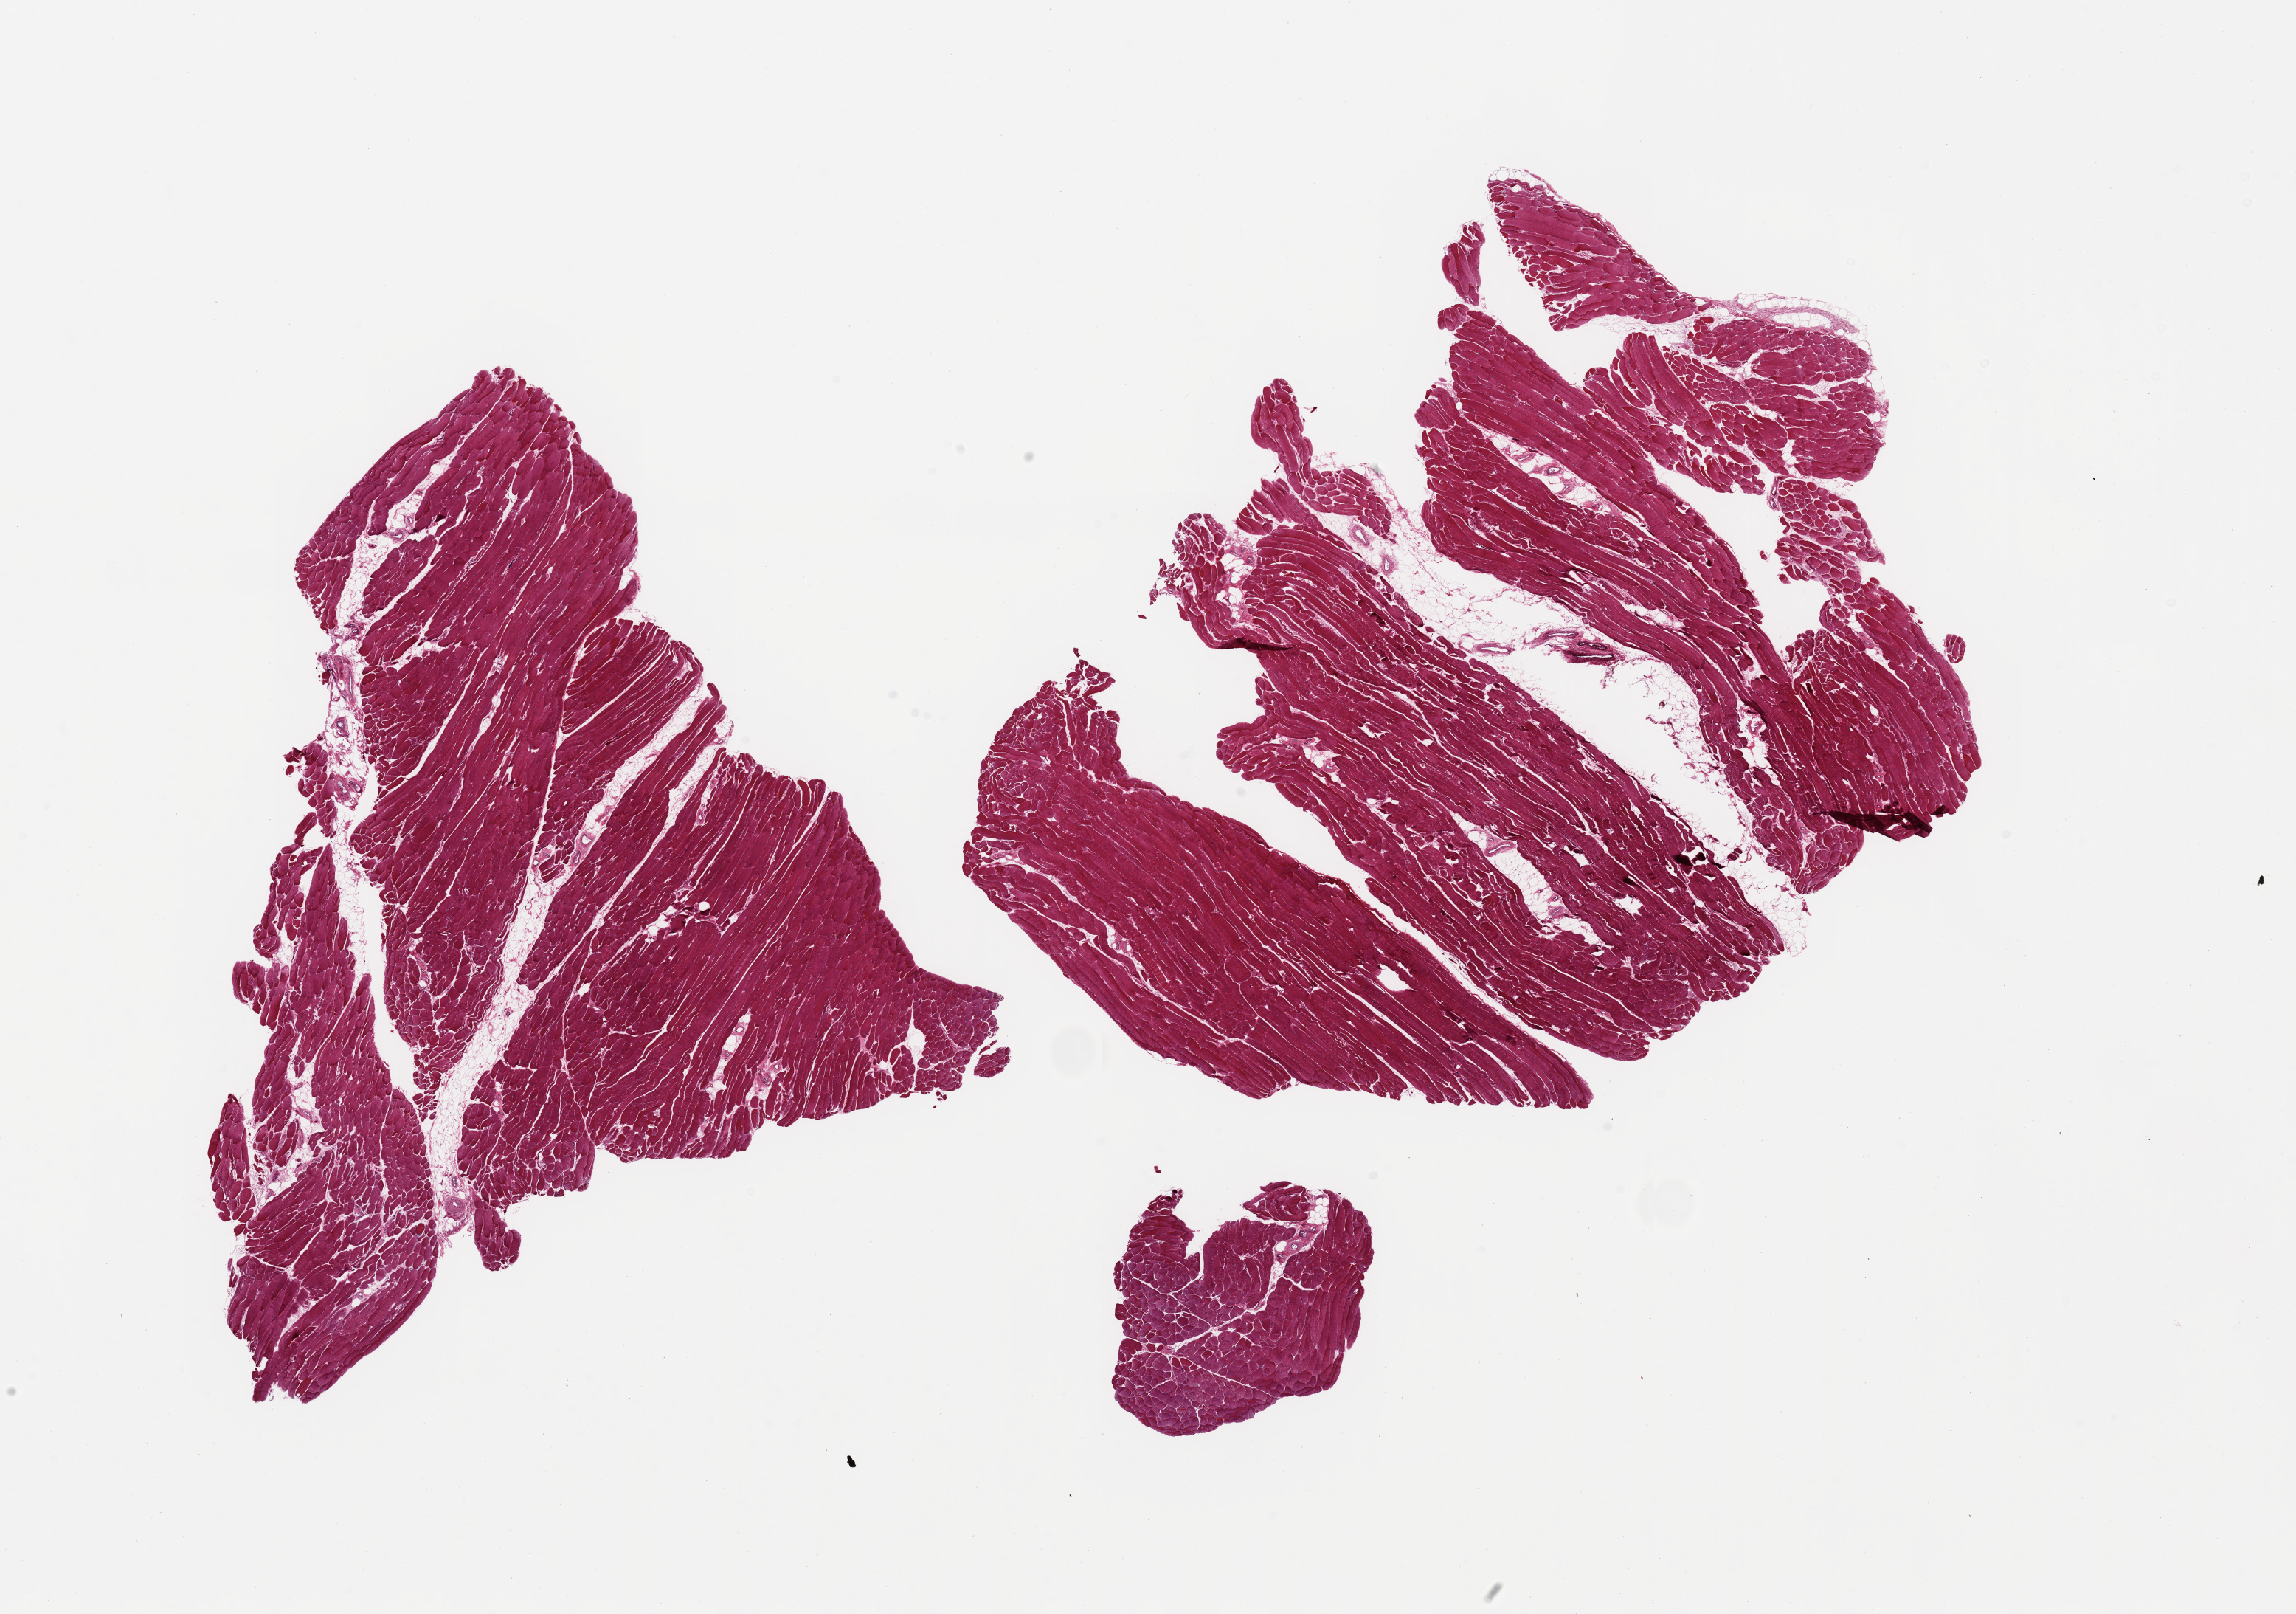
Whole-slide image, haematoxylin and eosin stain, brightfield — shown as a low-resolution overview of the whole scanned area (about 24.6 x 17.3 mm, from a 20x scan); PAXgene-fixed, paraffin-embedded tissue; section of skeletal muscle (target tissue); donor tissue sample. Male donor.
Reviewer comment on this tissue sample: 2 pieces, interstitial fat is ~5-10% of aliquot.